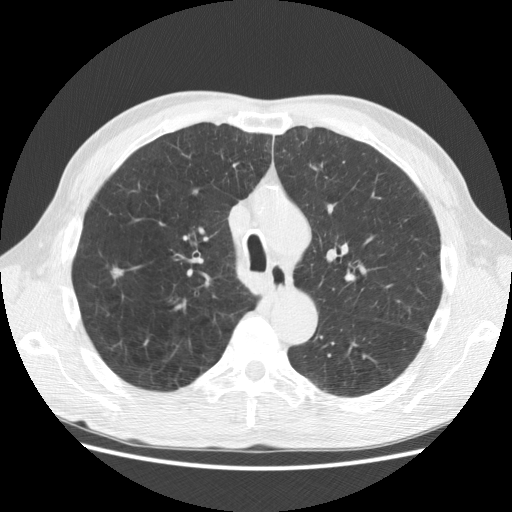
Chest CT (low-dose screening protocol), one axial image; baseline screening round; lung window (W 1500 / L -600 HU); 120 kVp. Male, age 62 years at enrolment.
Expert reader's lesion annotation, box from (x=102, y=260) to (x=136, y=292) px. The screening reader recorded 2 non-calcified nodules or masses ≥4 mm on this exam (right upper lobe, left lower lobe); which of them this box marks is not recorded. Official screen result: positive, change unspecified: nodule(s) >= 4 mm or enlarging nodule(s), mass(es), or other non-specific abnormalities suspicious for lung cancer. Lung cancer was diagnosed 183 days after this screen: bronchiolo-alveolar adenocarcinoma, NOS, right upper lobe, moderately differentiated (G2), stage IIA (AJCC 6th edition), 11 mm at pathology.